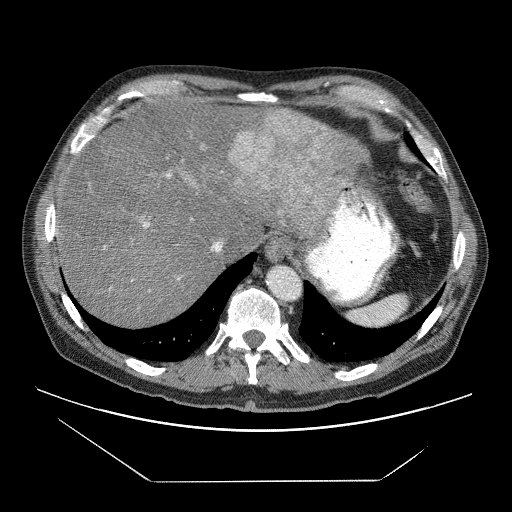
Contrast-enhanced abdominal CT (liver protocol), one axial slice. Position 56 of 83 along the scan axis. 120 kVp. Soft-tissue window (W 400 / L 40 HU). 2.5 mm slice thickness. 512 × 512 image matrix. Case-level facts recorded for this patient, not image findings: diagnosis: hepatocellular carcinoma (patient treated with transarterial chemoembolisation; whether this scan precedes or follows treatment is not stated here); TNM stage (as recorded): Stage-IVB; Child-Pugh class: B; tumour differentiation: poorly differentiated; tumour nodularity: uninodular.
Outlined on this slice (semi-automatically segmented with operator editing):
- liver parenchyma outside the tumour (the mass and vessels are separate outlines, so this box may not span the whole liver): bounding box (x1, y1, x2, y2) in pixels: (54, 102, 368, 326)
- mass: (228, 108, 365, 232)
- liver vessels: (54, 145, 241, 292)